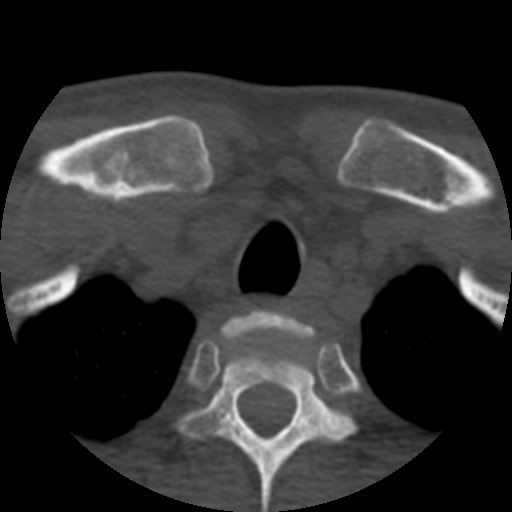
CT including the spine, one axial slice; position 434 of 508 along the scan axis; bone window (W 1800 / L 400 HU); 1.25 mm slice thickness; 512 × 512 image matrix, field of view 160 × 160 mm. Patient age 57 years. From the clinical record (not read from this slice): primary cancer: prostate.
Outlined on this slice (semi-automatic segmentation, software-assisted and operator-edited):
- T1 vertebra: bounding box <223,313,314,350> (left, top, right, bottom; pixels)
- T2 vertebra: <172,329,354,512>